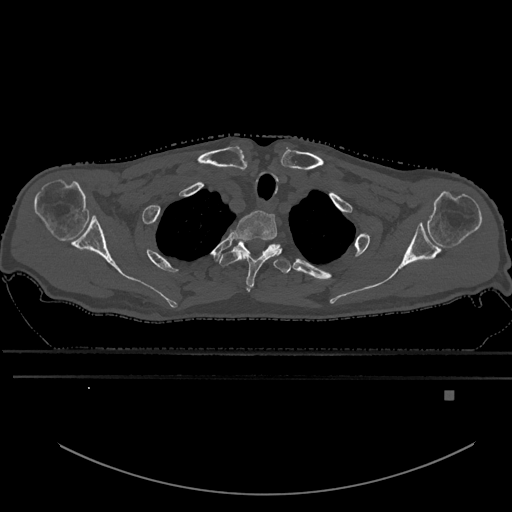
CT including the spine, one axial slice. Bone window (W 1800 / L 400 HU). 0.5 mm slice thickness. 512 × 512 image matrix. Patient: male, 82 years. Case-level facts recorded for this patient, not image findings: primary cancer: prostate; vertebrae with lytic lesions (as recorded): T11, T9, T8, T2.
Structures marked on this image (semi-automatic segmentation, software-assisted and operator-edited):
- T1 vertebra: box from (x=234, y=210) to (x=279, y=292) px
- T2 vertebra: (x=219, y=239)–(x=287, y=272)